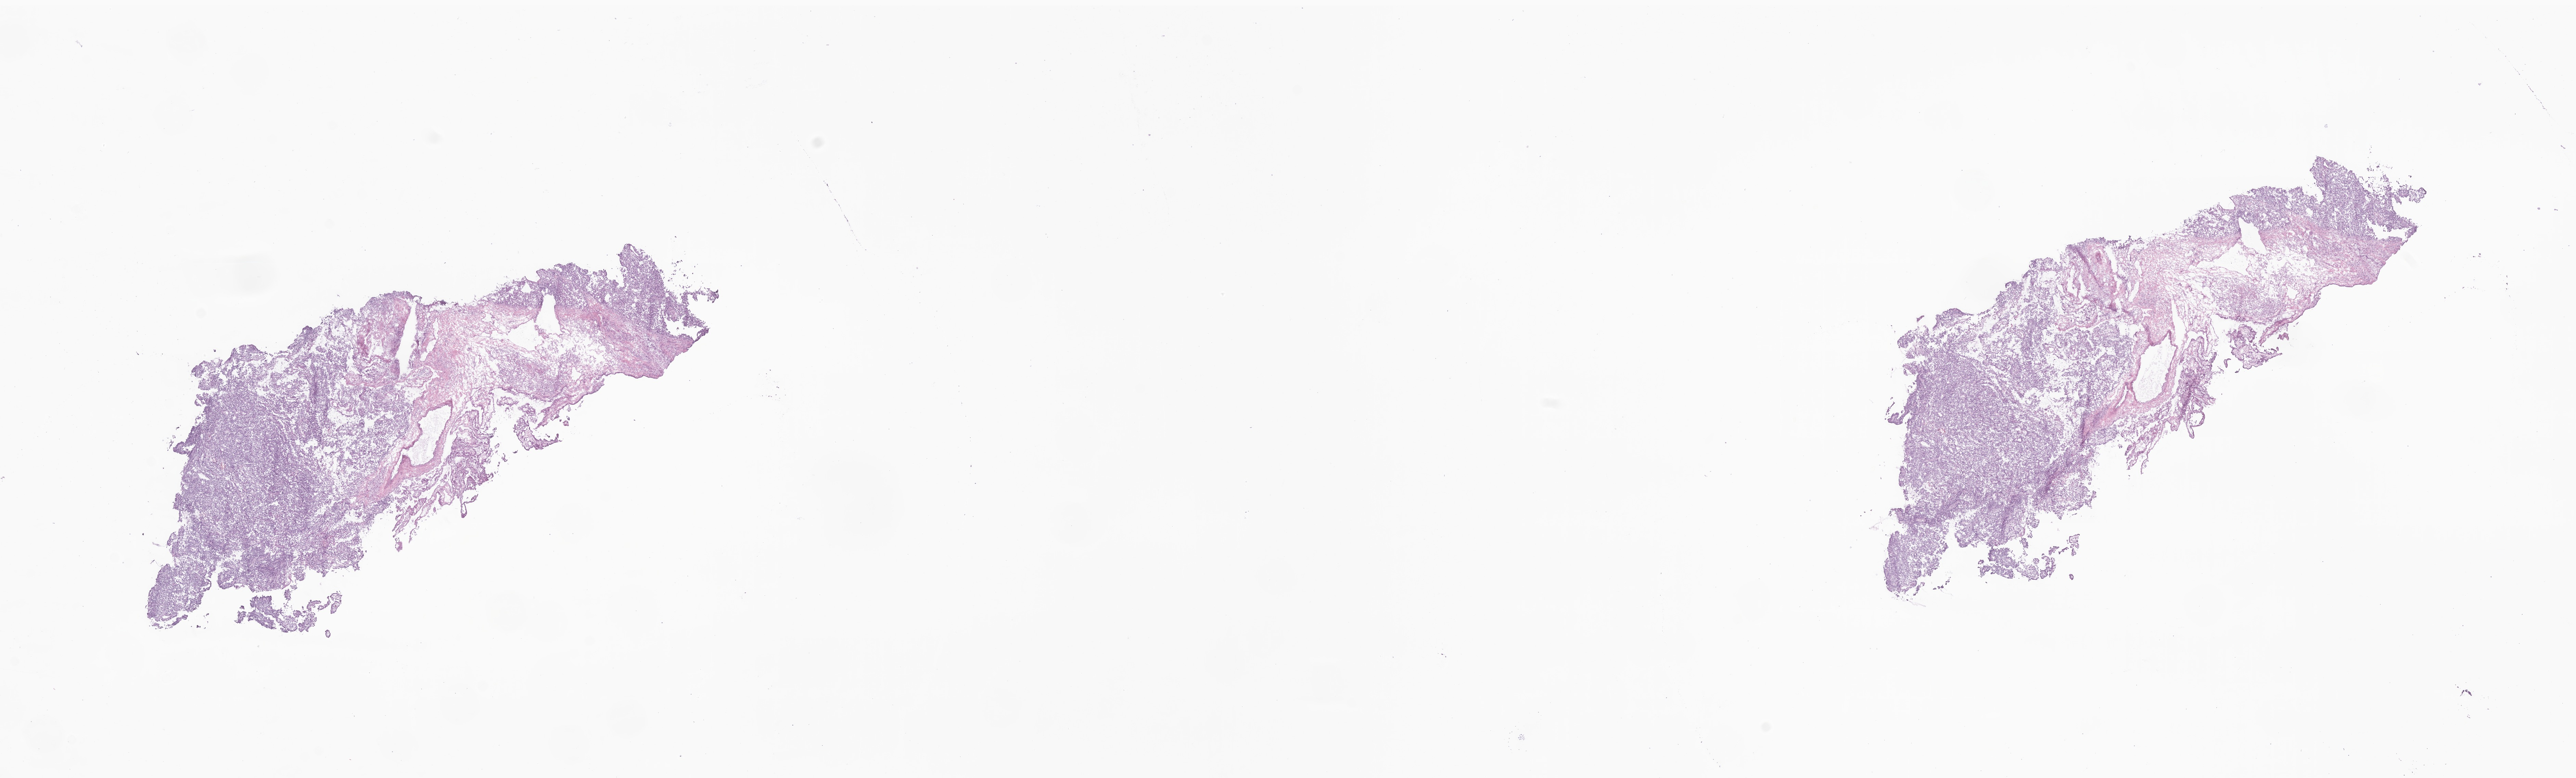
Digitized haematoxylin and eosin-stained section of tumor tissue from the brain — shown as a low-resolution overview of the whole scanned area (about 31.7 x 9.6 mm); frozen section (OCT-embedded). Patient female; age 832 days (about 2.3 years).
* diagnosis (ICD-O-3 morphology term): Choroid plexus carcinoma